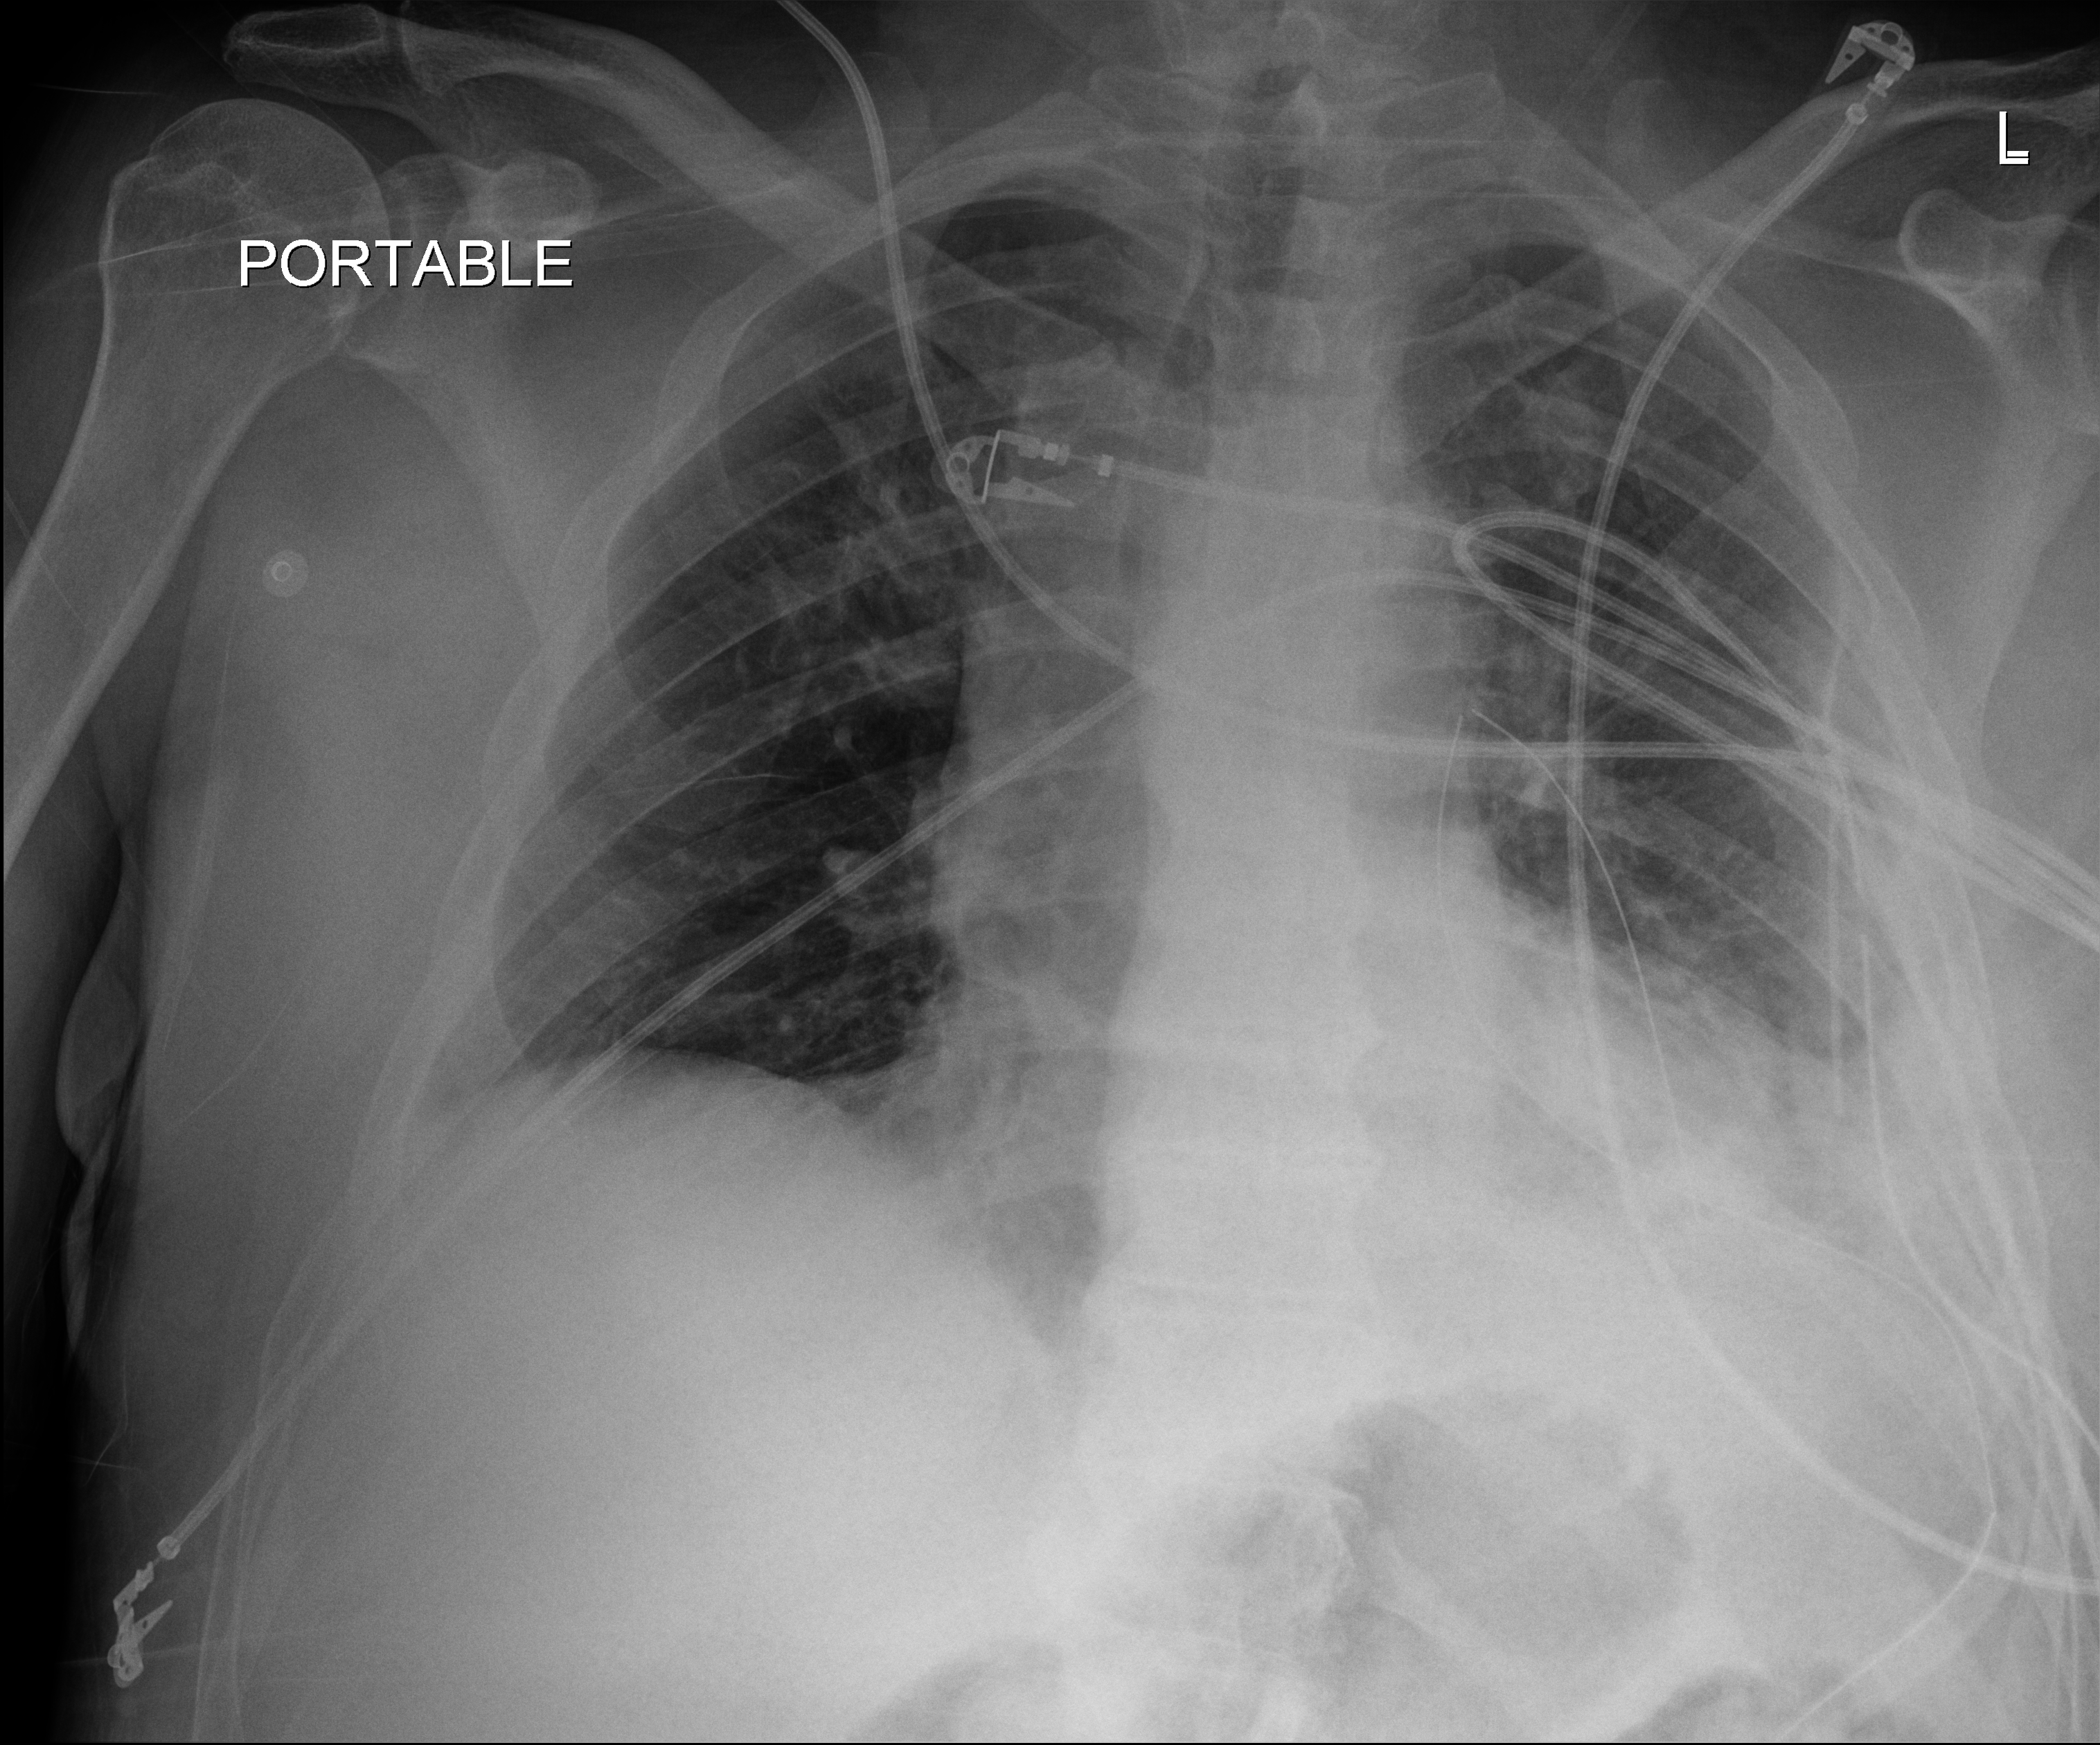
Chest X-ray (portable), anteroposterior (AP) projection. Patient hospitalised with COVID-19; male, aged 18–59 years.
Admission-level facts for this patient (not findings on this image; timing relative to this image not recorded): mechanically ventilated during this hospital stay: no.